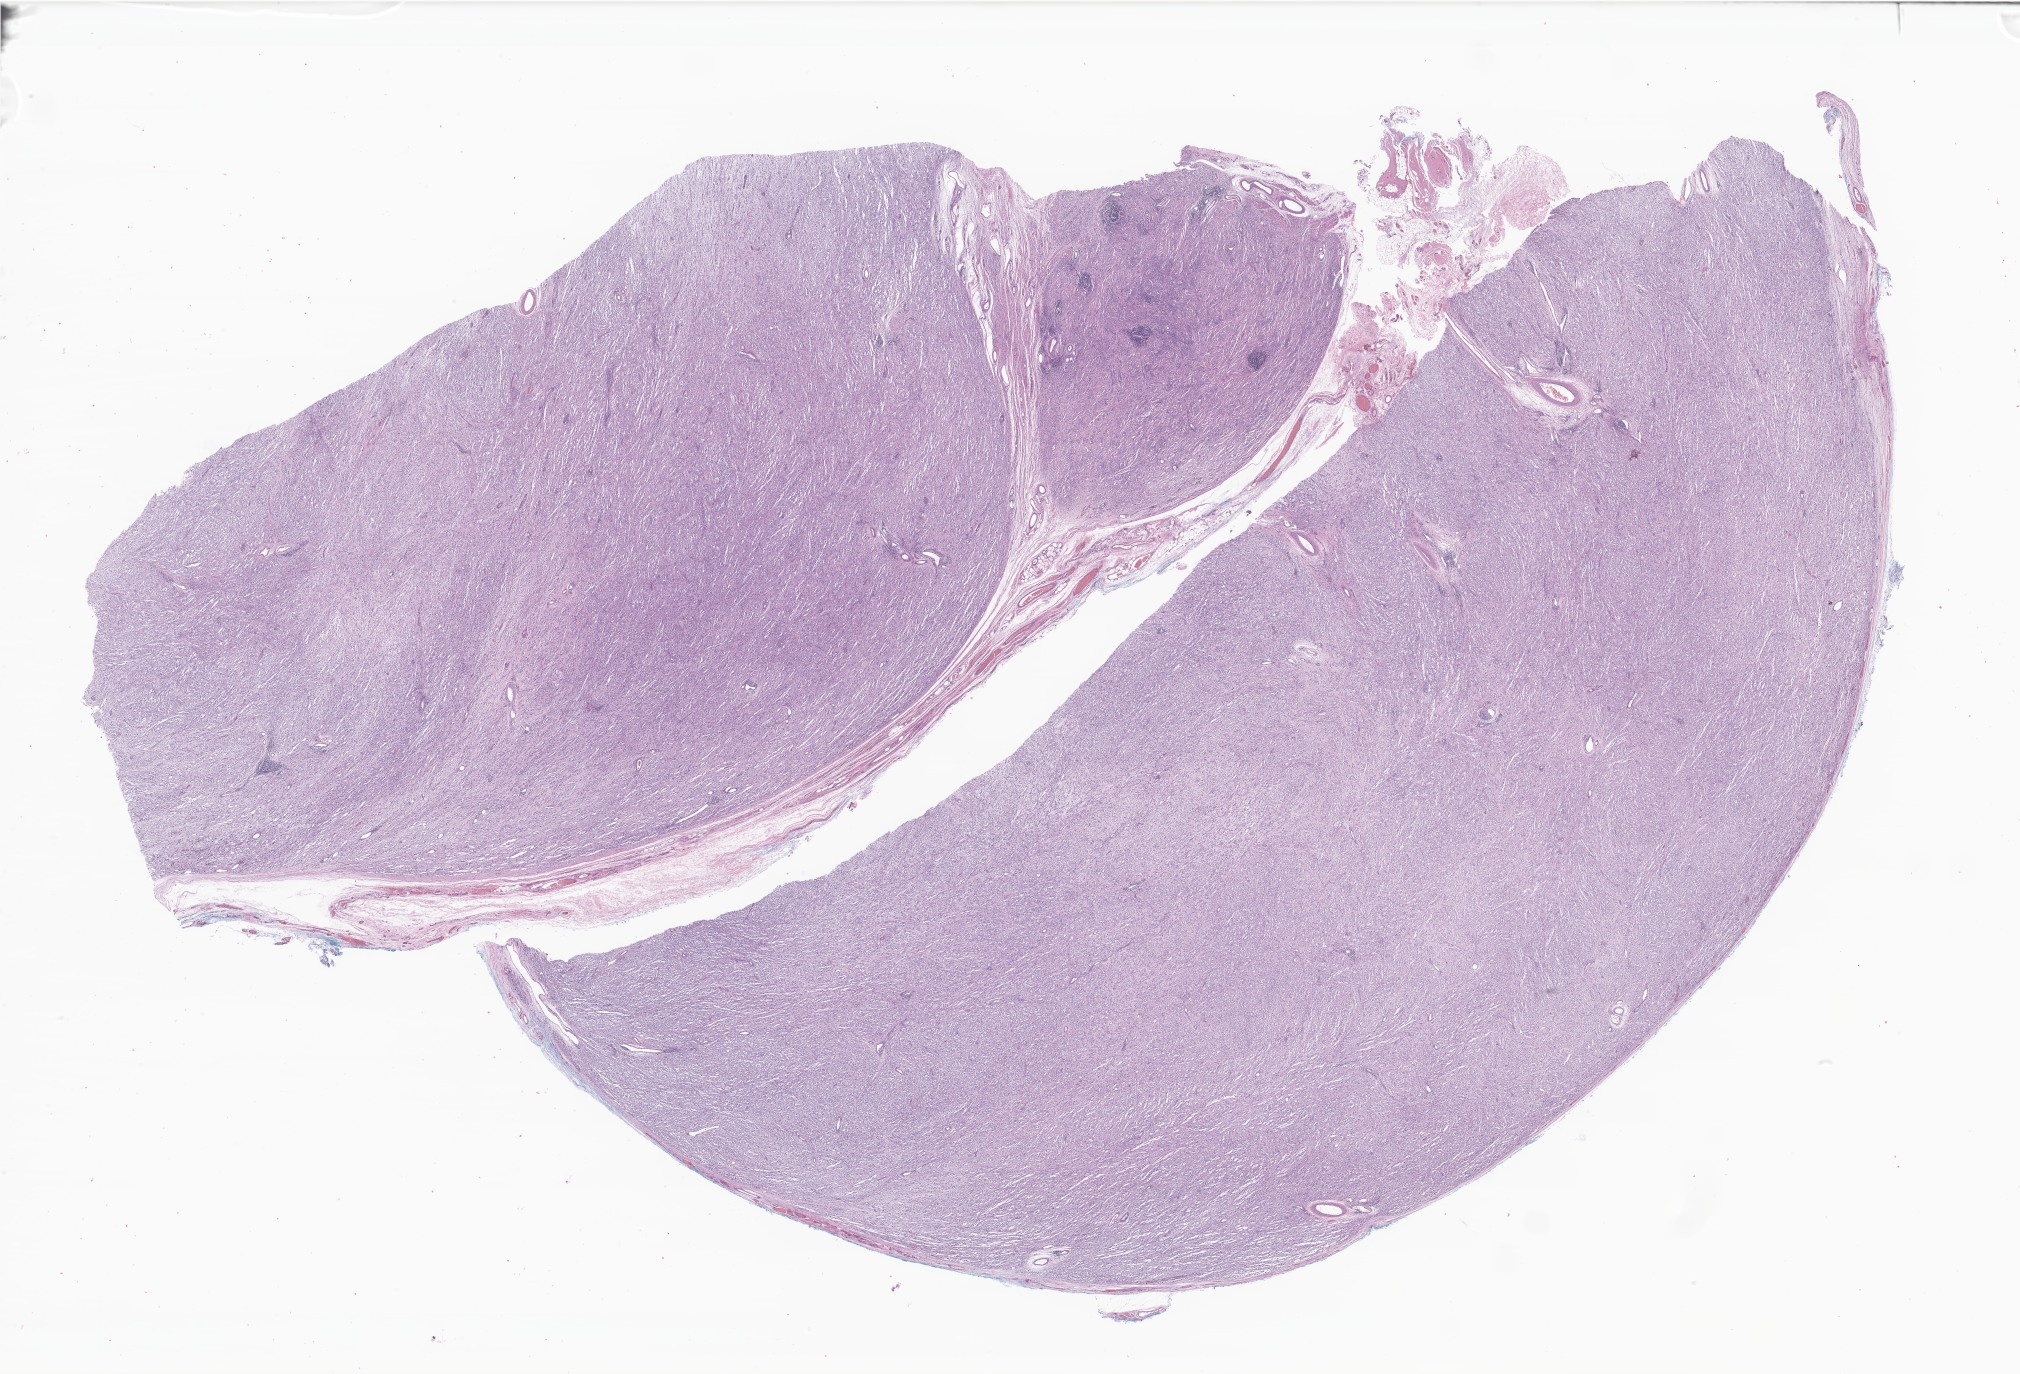
Digitized H&E-stained section of tumor tissue from the descended testis — low-resolution overview of the scanned area, about 34.1 x 23.2 mm. Formalin-fixed, paraffin-embedded (FFPE) tissue. Patient: male, age 44 months.
Diagnosis: Embryonal rhabdomyosarcoma, NOS.